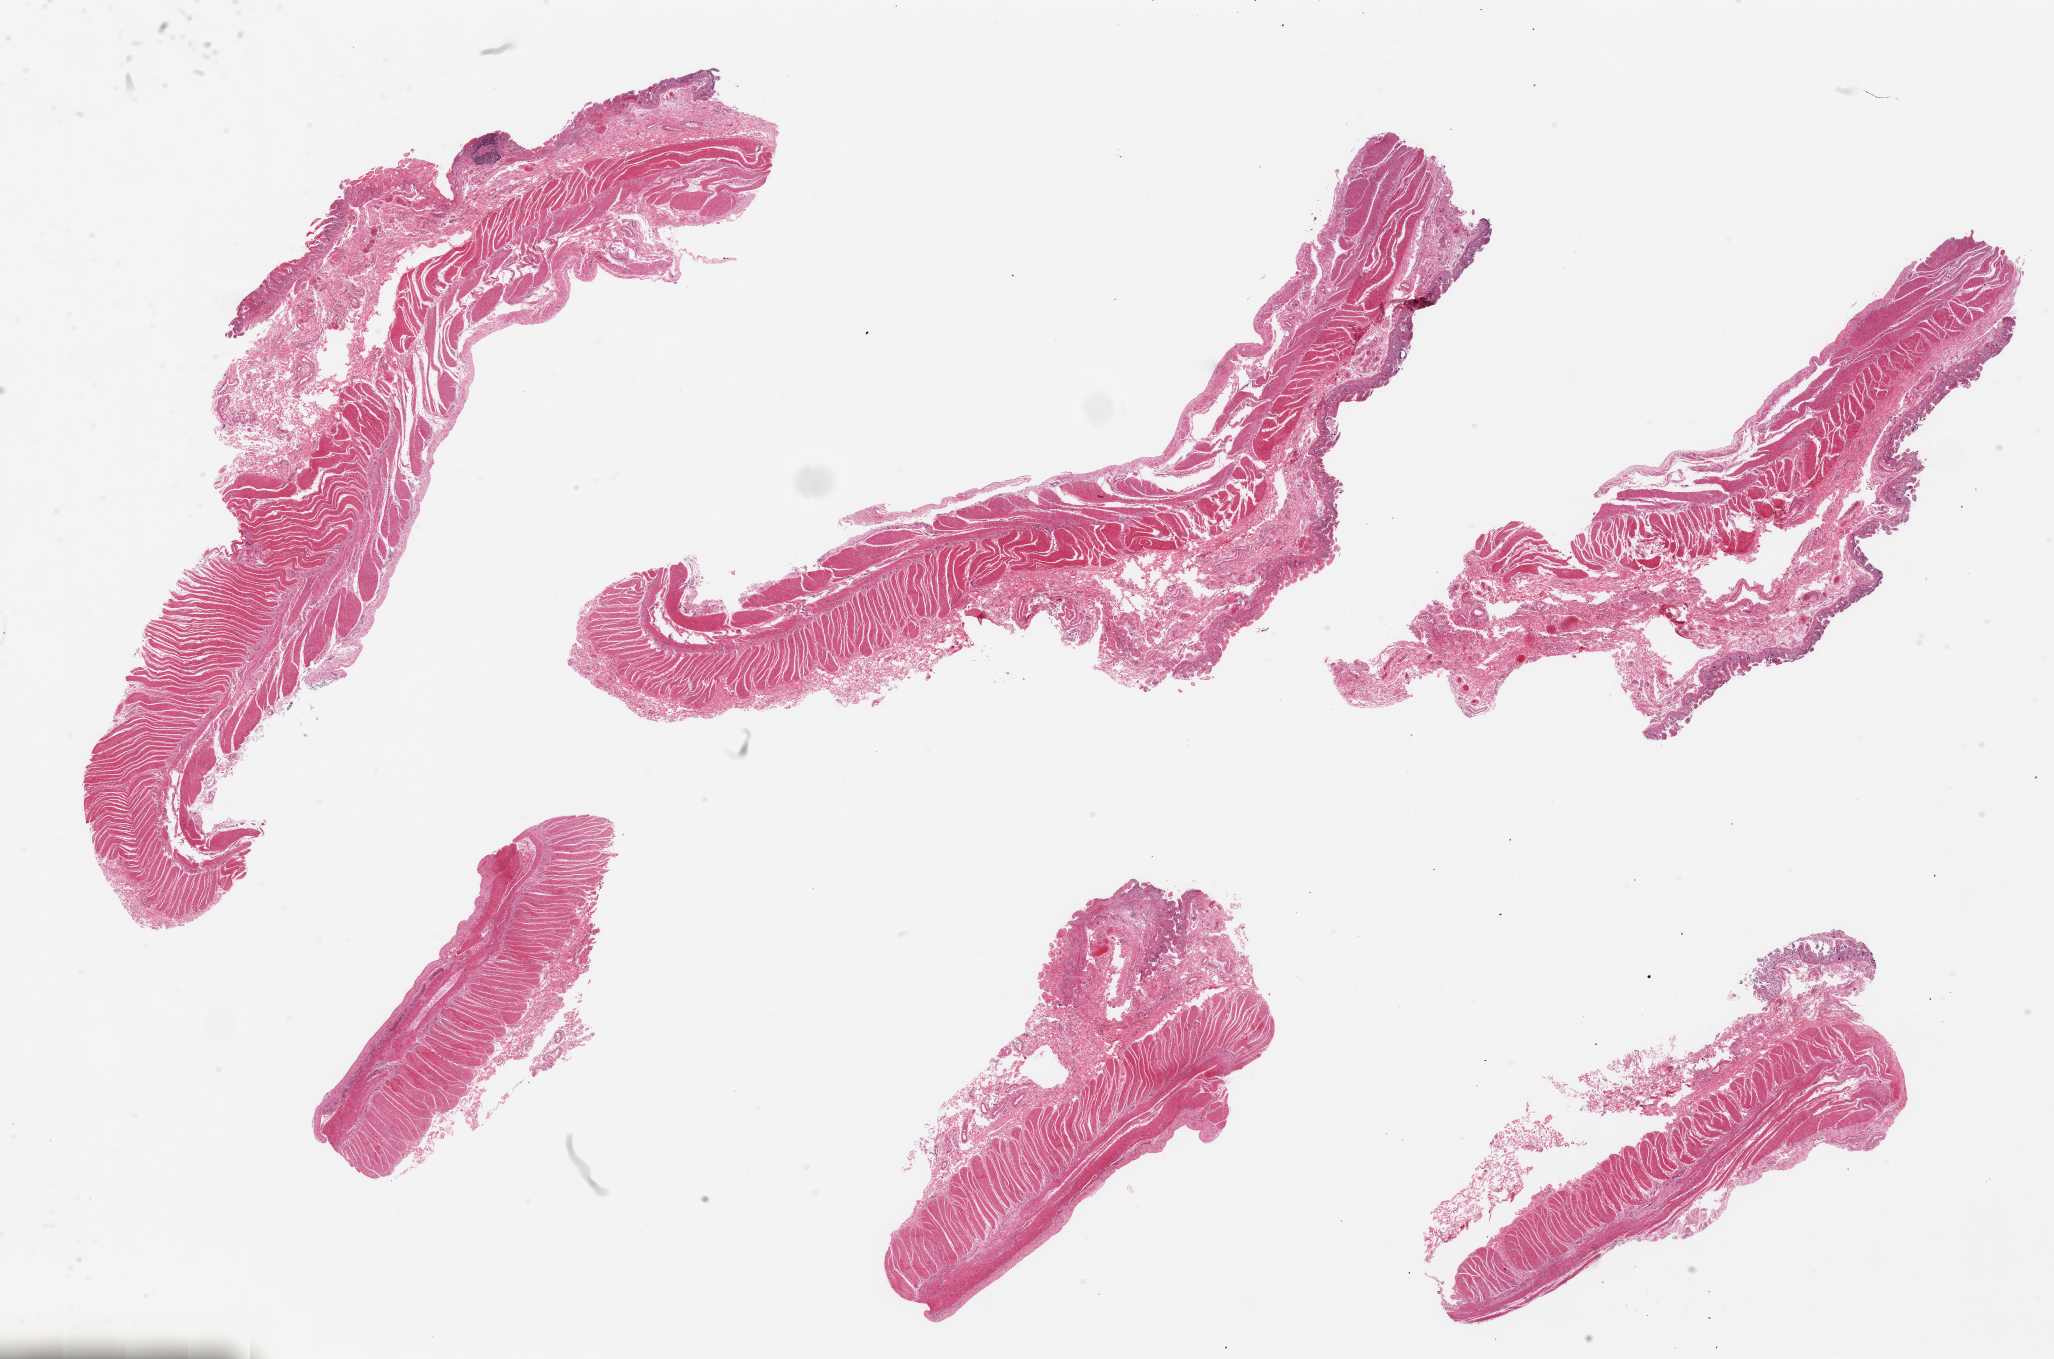
Whole-slide image, H&E stain, low-resolution overview of the scanned area, about 32.5 x 21.5 mm (slide scanned at 20x), PAXgene-fixed paraffin-embedded (PFPE) section, sampled site (target tissue): ileum, tissue donor sample. Donor sex: male.
* review note (as recorded): 6 pieces, advanced autolysis, less than 1% target lymphoid aggregates